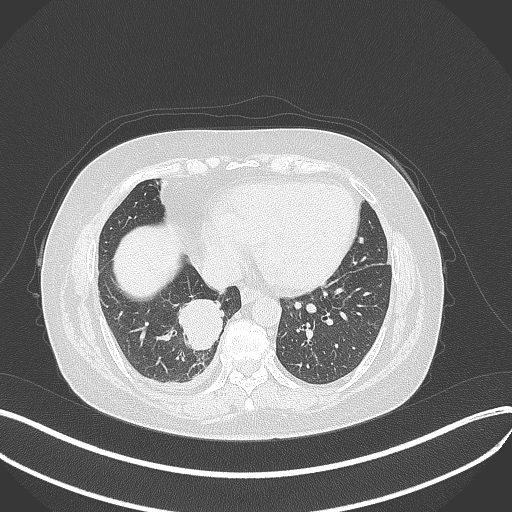
Chest CT, one axial slice. Slice 119 of 381 in the series (ordered by position). 120 kVp. Lung window (W 1500 / L -600 HU). 512 × 512 image matrix, field of view 400 × 400 mm. Patient: female, 56 years. Case-level facts recorded for this patient, not image findings: clinical TNM (as recorded): T2b N1 M0.
Structures marked on this image (bounding box drawn by a radiologist):
- lung tumour (recorded histology: small cell carcinoma): box from (x=177, y=296) to (x=226, y=353) px